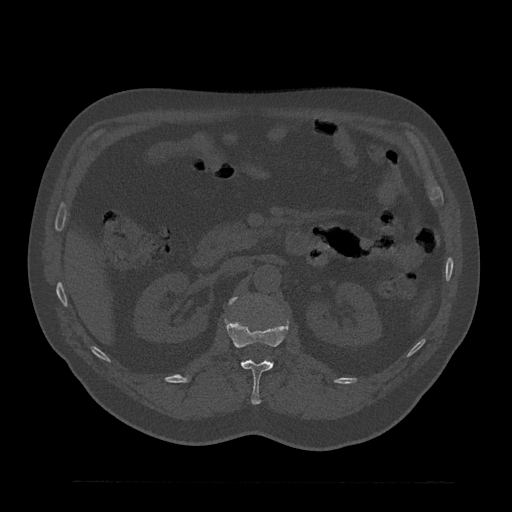
CT including the spine, one axial slice; slice 152 of 797 in the series (ordered by position); 120 kVp; bone window (W 1800 / L 400 HU); 512 × 512 image matrix, field of view 430 × 430 mm. Male patient, age 61 years. Case-level facts recorded for this patient, not image findings: primary cancer: prostate.
Annotated regions visible in this slice (semi-automatic segmentation, software-assisted and operator-edited):
- L1 vertebra: bounding box <225,319,288,405> (left, top, right, bottom; pixels)
- L2 vertebra: <230,297,236,304>